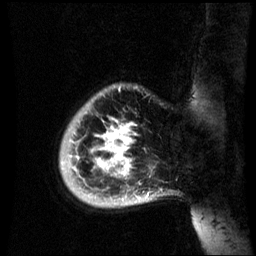
Breast MRI (dynamic contrast-enhanced), one sagittal slice. Position 8 of 60 along the scan axis. Dynamic contrast-enhanced series, image 2 of 3 at this slice position (ordered by acquisition). 1.5 T. TE 4.2 ms, TR 8.9 ms. 2.6 mm slice thickness. 256 × 256 image matrix, field of view 220 × 220 mm. Patient: female, 35 years. Case-level facts recorded for this patient, not image findings: setting: breast cancer imaged before/during neoadjuvant chemotherapy; receptor status: HR-positive, HER2-negative.
Annotated regions visible in this slice (semi-automatic segmentation, software-assisted and operator-edited):
- analysis volume of interest (the breast-tissue region the enhancement analysis was run in; not a lesion): bounding box [x1, y1, x2, y2] px = [59, 84, 164, 209]
- tumour enhancement mask (voxels above the 70 % enhancement threshold inside the analysis volume of interest): [97, 118, 133, 177]